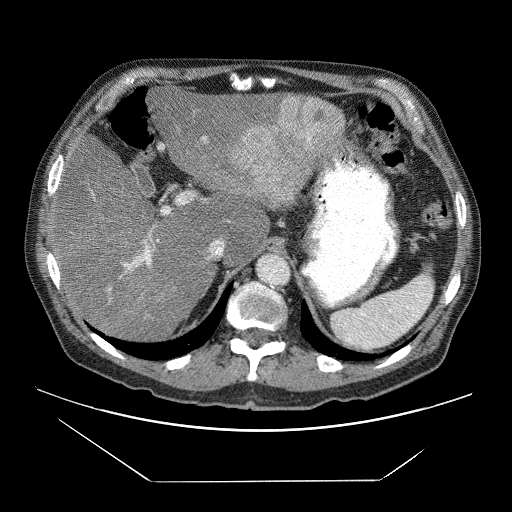
Contrast-enhanced abdominal CT (liver protocol), one axial slice. Slice 47 of 83 in the series (ordered by position). 120 kVp. Soft-tissue window (W 400 / L 40 HU). 2.5 mm slice thickness. 512 × 512 image matrix. Case-level facts recorded for this patient, not image findings: diagnosis: hepatocellular carcinoma (patient treated with transarterial chemoembolisation; whether this scan precedes or follows treatment is not stated here); TNM stage (as recorded): Stage-IVB; Child-Pugh class: B; tumour differentiation: poorly differentiated; tumour nodularity: uninodular.
Outlined on this slice (semi-automatically segmented with operator editing):
- liver parenchyma outside the tumour (the mass and vessels are separate outlines, so this box may not span the whole liver): bounding box (x1, y1, x2, y2) in pixels: (48, 76, 344, 338)
- mass: (230, 96, 345, 204)
- liver vessels: (92, 136, 212, 301)